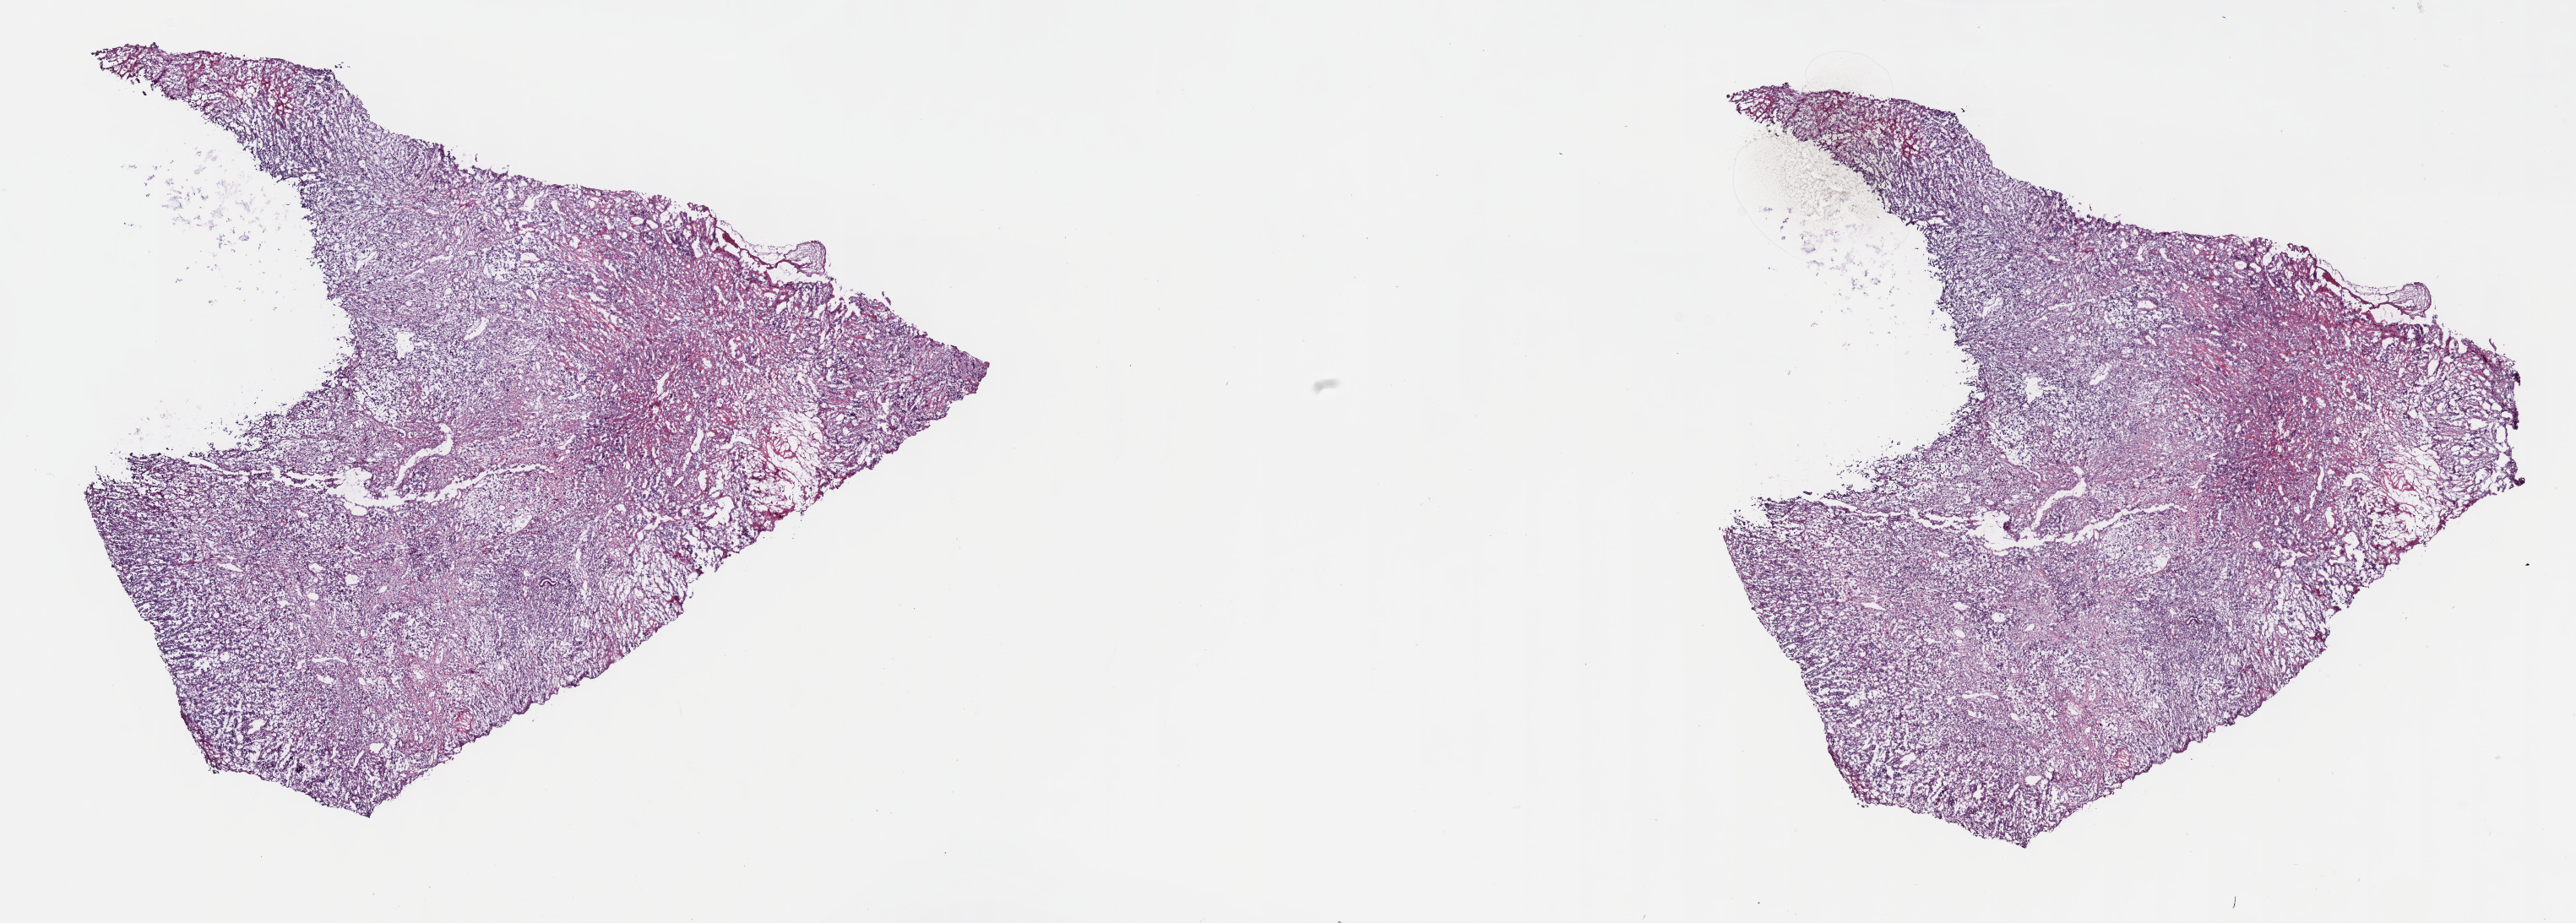
Digitized H&E-stained tissue section (whole slide), shown as a low-resolution overview of the whole scanned area (about 24.7 x 8.8 mm, slide scanned at 40x); frozen section; sample: primary tumour, head and neck. Male, age 60 years at initial diagnosis. Histologic grade: G2 (moderately differentiated). Slide review estimates, as recorded: tumour cells 75%, tumour nuclei 75%, normal cells 0%, stromal cells 25%, necrosis 0%. Infiltration values recorded for this section: lymphocyte infiltration 10%, monocyte infiltration 0%, neutrophil infiltration 0%.
AJCC pathologic stage: IVA (7th edition). Laterality: right. Pathologic diagnosis: Squamous cell carcinoma, NOS (tongue, NOS).